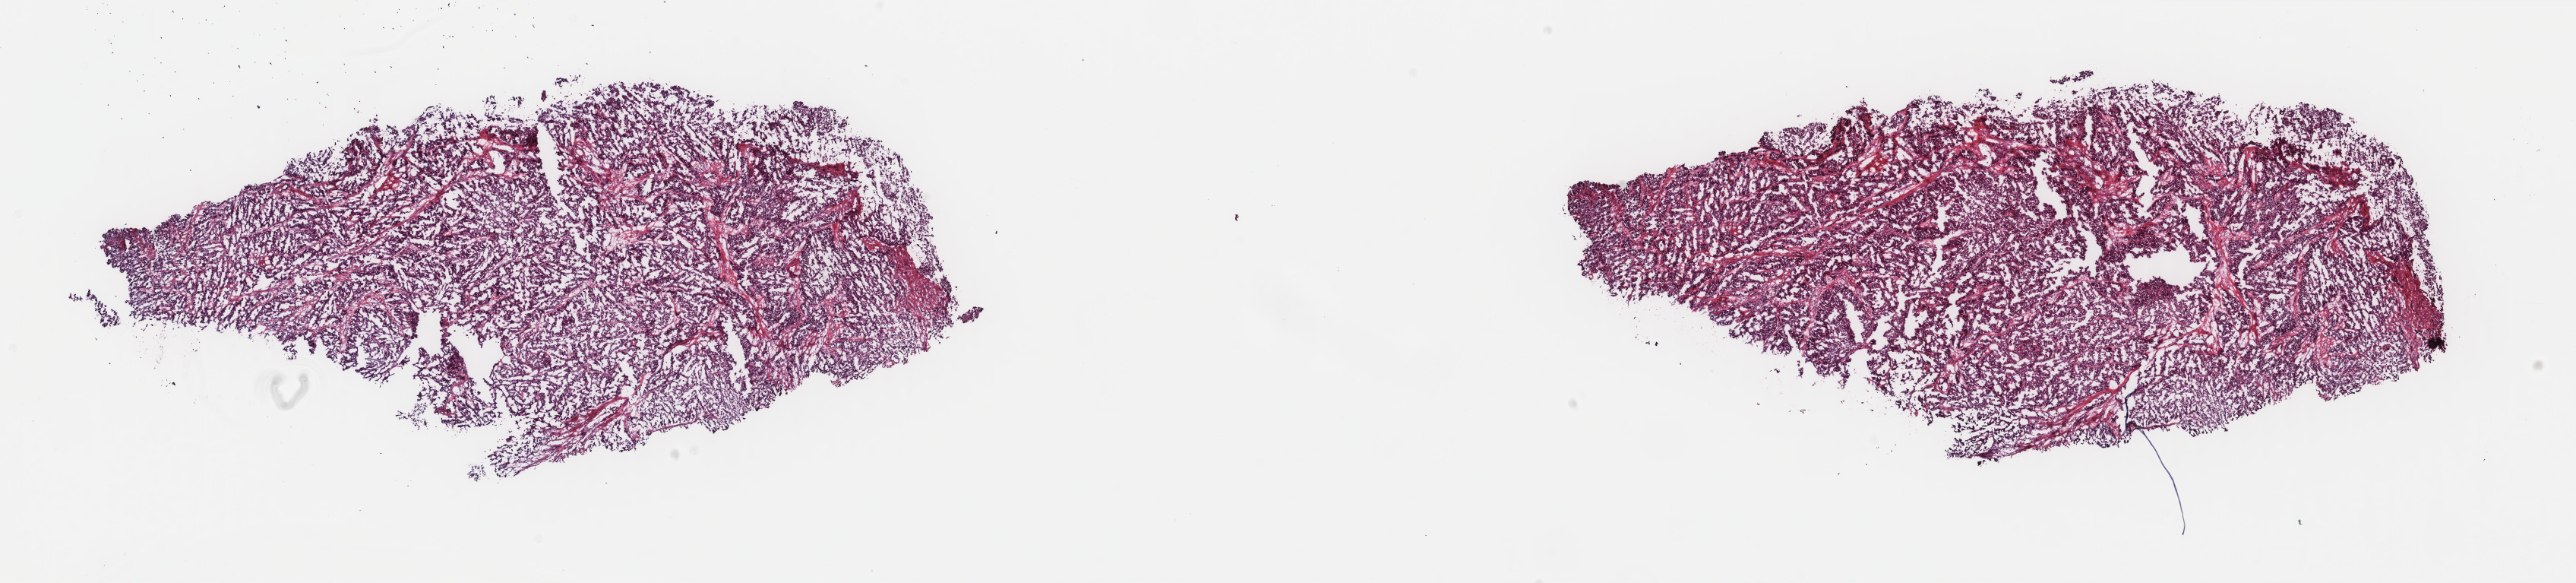
Hematoxylin and eosin (H&E) stained whole-slide image — shown as a low-resolution overview of the whole scanned area (about 26.9 x 6.1 mm, acquisition: 40x scan); frozen section from the top of the tissue portion; sample: primary tumour, bladder. Patient: female, age at initial diagnosis 61 years. Histologic grade: high grade. Pathologist review of this section (percent, as recorded): tumour cells 75%, tumour nuclei 90%, normal cells 0%, stromal cells 23%, necrosis 2%. Inflammatory infiltration, as recorded: lymphocyte infiltration 1%, monocyte infiltration 0%, neutrophil infiltration 0%.
AJCC pathologic stage: IV. Diagnosis: Transitional cell carcinoma (lateral wall of bladder).